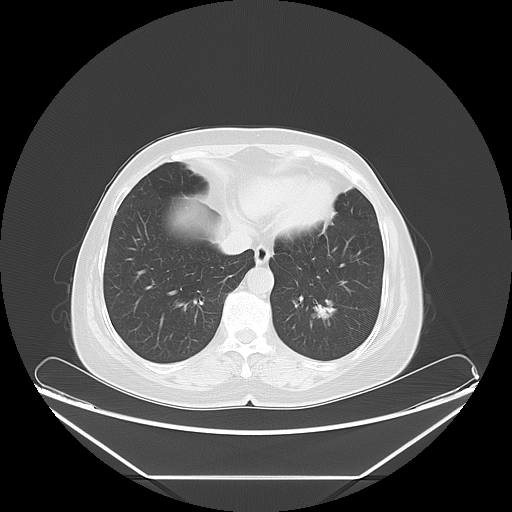
Chest CT, one axial slice; position 18 of 61 along the scan axis; lung window (W 1500 / L -600 HU); 5 mm slice thickness; 512 × 512 image matrix, field of view 451 × 451 mm. Patient: female, 63 years. From the clinical record (not read from this slice): clinical TNM (as recorded): T1c N0 M0.
Annotated regions visible in this slice (rectangle marked by the reading radiologist):
- lung tumour (recorded histology: adenocarcinoma): box from (x=312, y=296) to (x=336, y=321) px